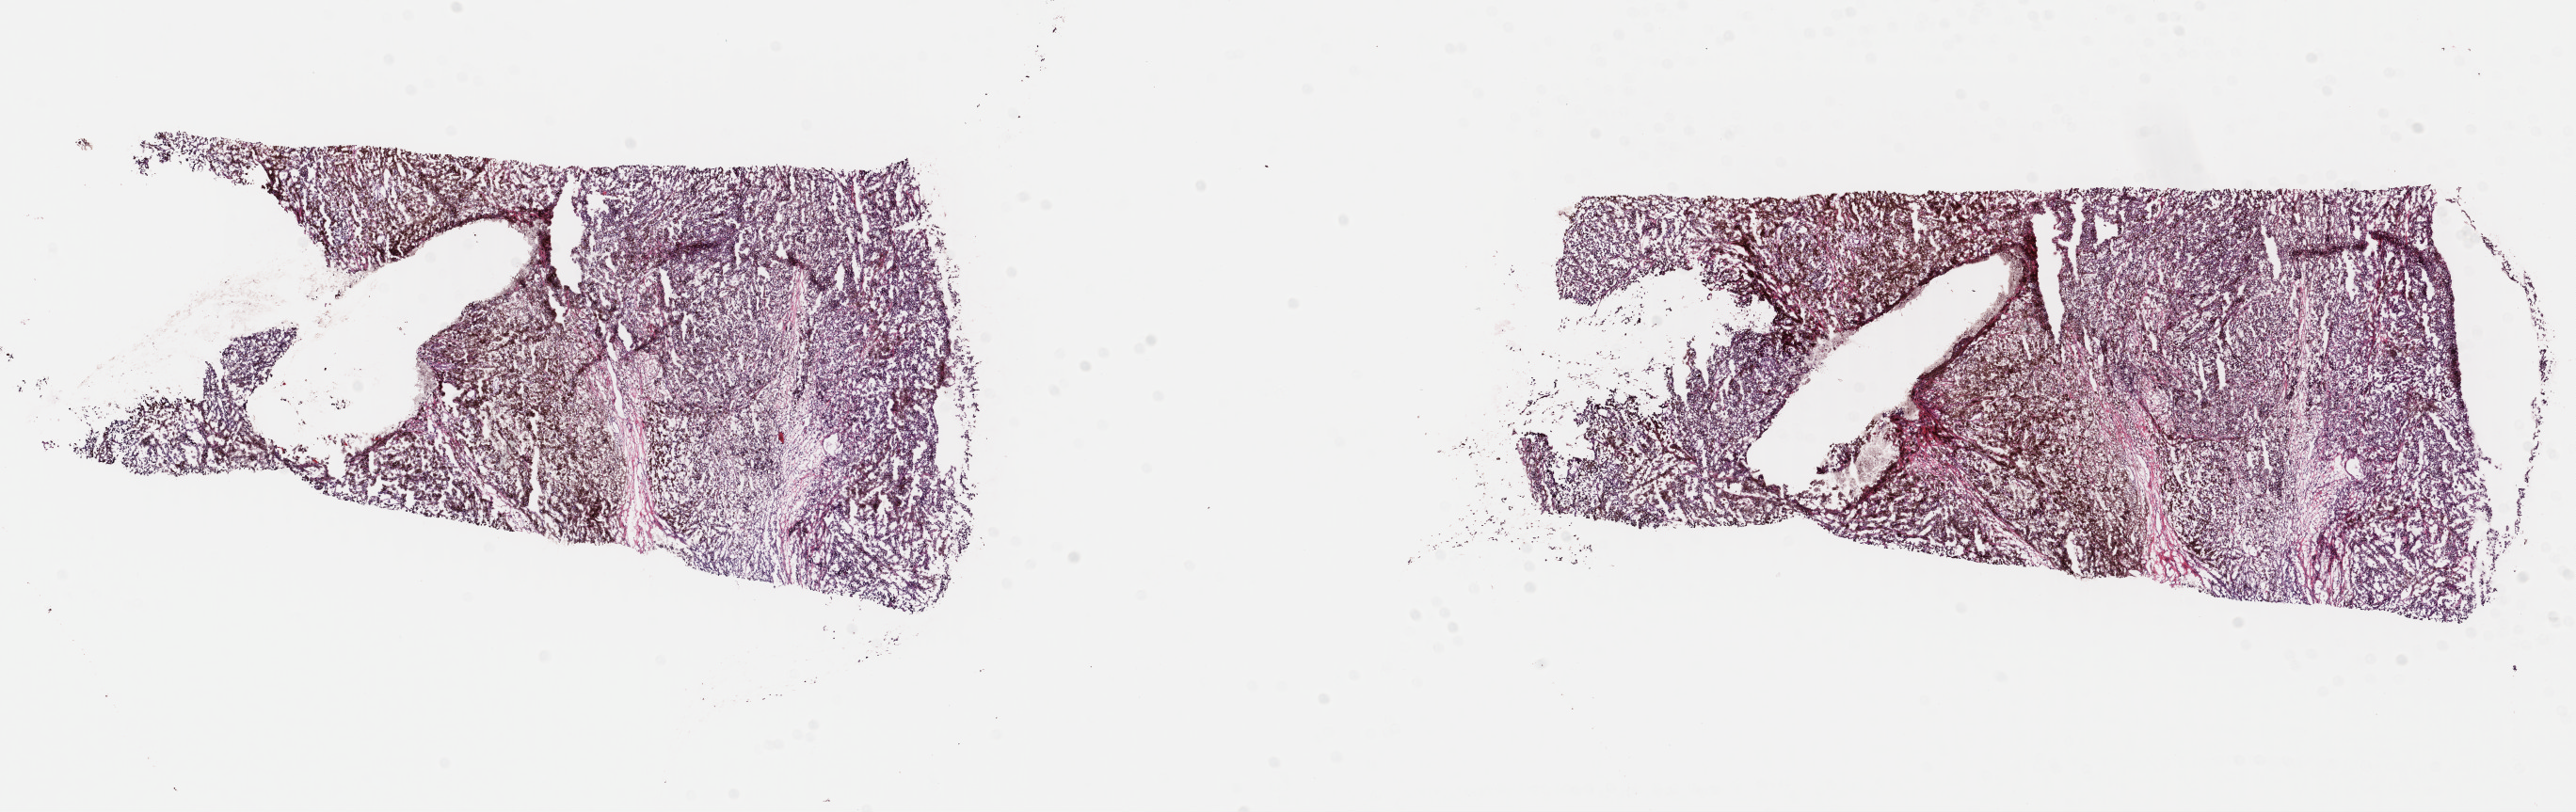
Digitized H&E-stained tissue section (whole slide), whole scanned area (about 21.5 x 6.8 mm, from a 40x scan) shown as a low-resolution overview. Frozen section from the top of the tissue portion. Primary tumour sample from the skin. Male, age 57 years at initial diagnosis. Pathologist review of this section (percent, as recorded): tumour cells 85%, tumour nuclei 85%, normal cells 0%, stromal cells 15%, necrosis 0%. Infiltration values recorded for this section: lymphocyte infiltration 2%, monocyte infiltration 3%, neutrophil infiltration 0%.
• pathologic diagnosis: Malignant melanoma, NOS